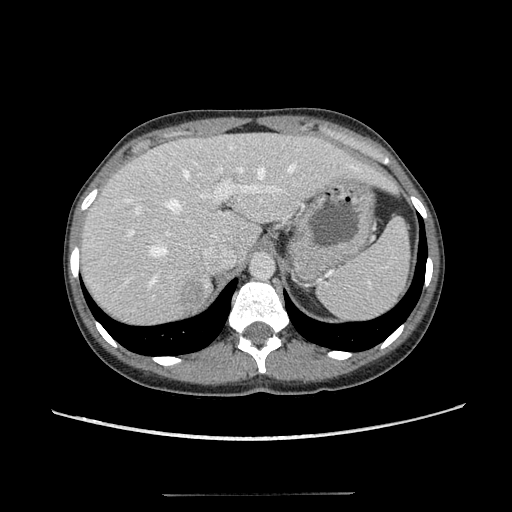
Contrast-enhanced abdominal CT, one axial slice; slice 85 of 117 in the series (ordered by position); reconstruction kernel STANDARD; soft-tissue window (W 400 / L 40 HU); 512 × 512 image matrix. Patient: female, 35 years. From the clinical record (not read from this slice): diagnosis: adrenocortical carcinoma; tumour side: right adrenal; tumour size at pathology: 3 cm; Ki-67 index: 21 %; stage (as recorded): 3.
Outlined on this slice (semi-automatic segmentation, software-assisted and operator-edited):
- mass: bounding box (x1, y1, x2, y2) in pixels: (178, 280, 207, 307)